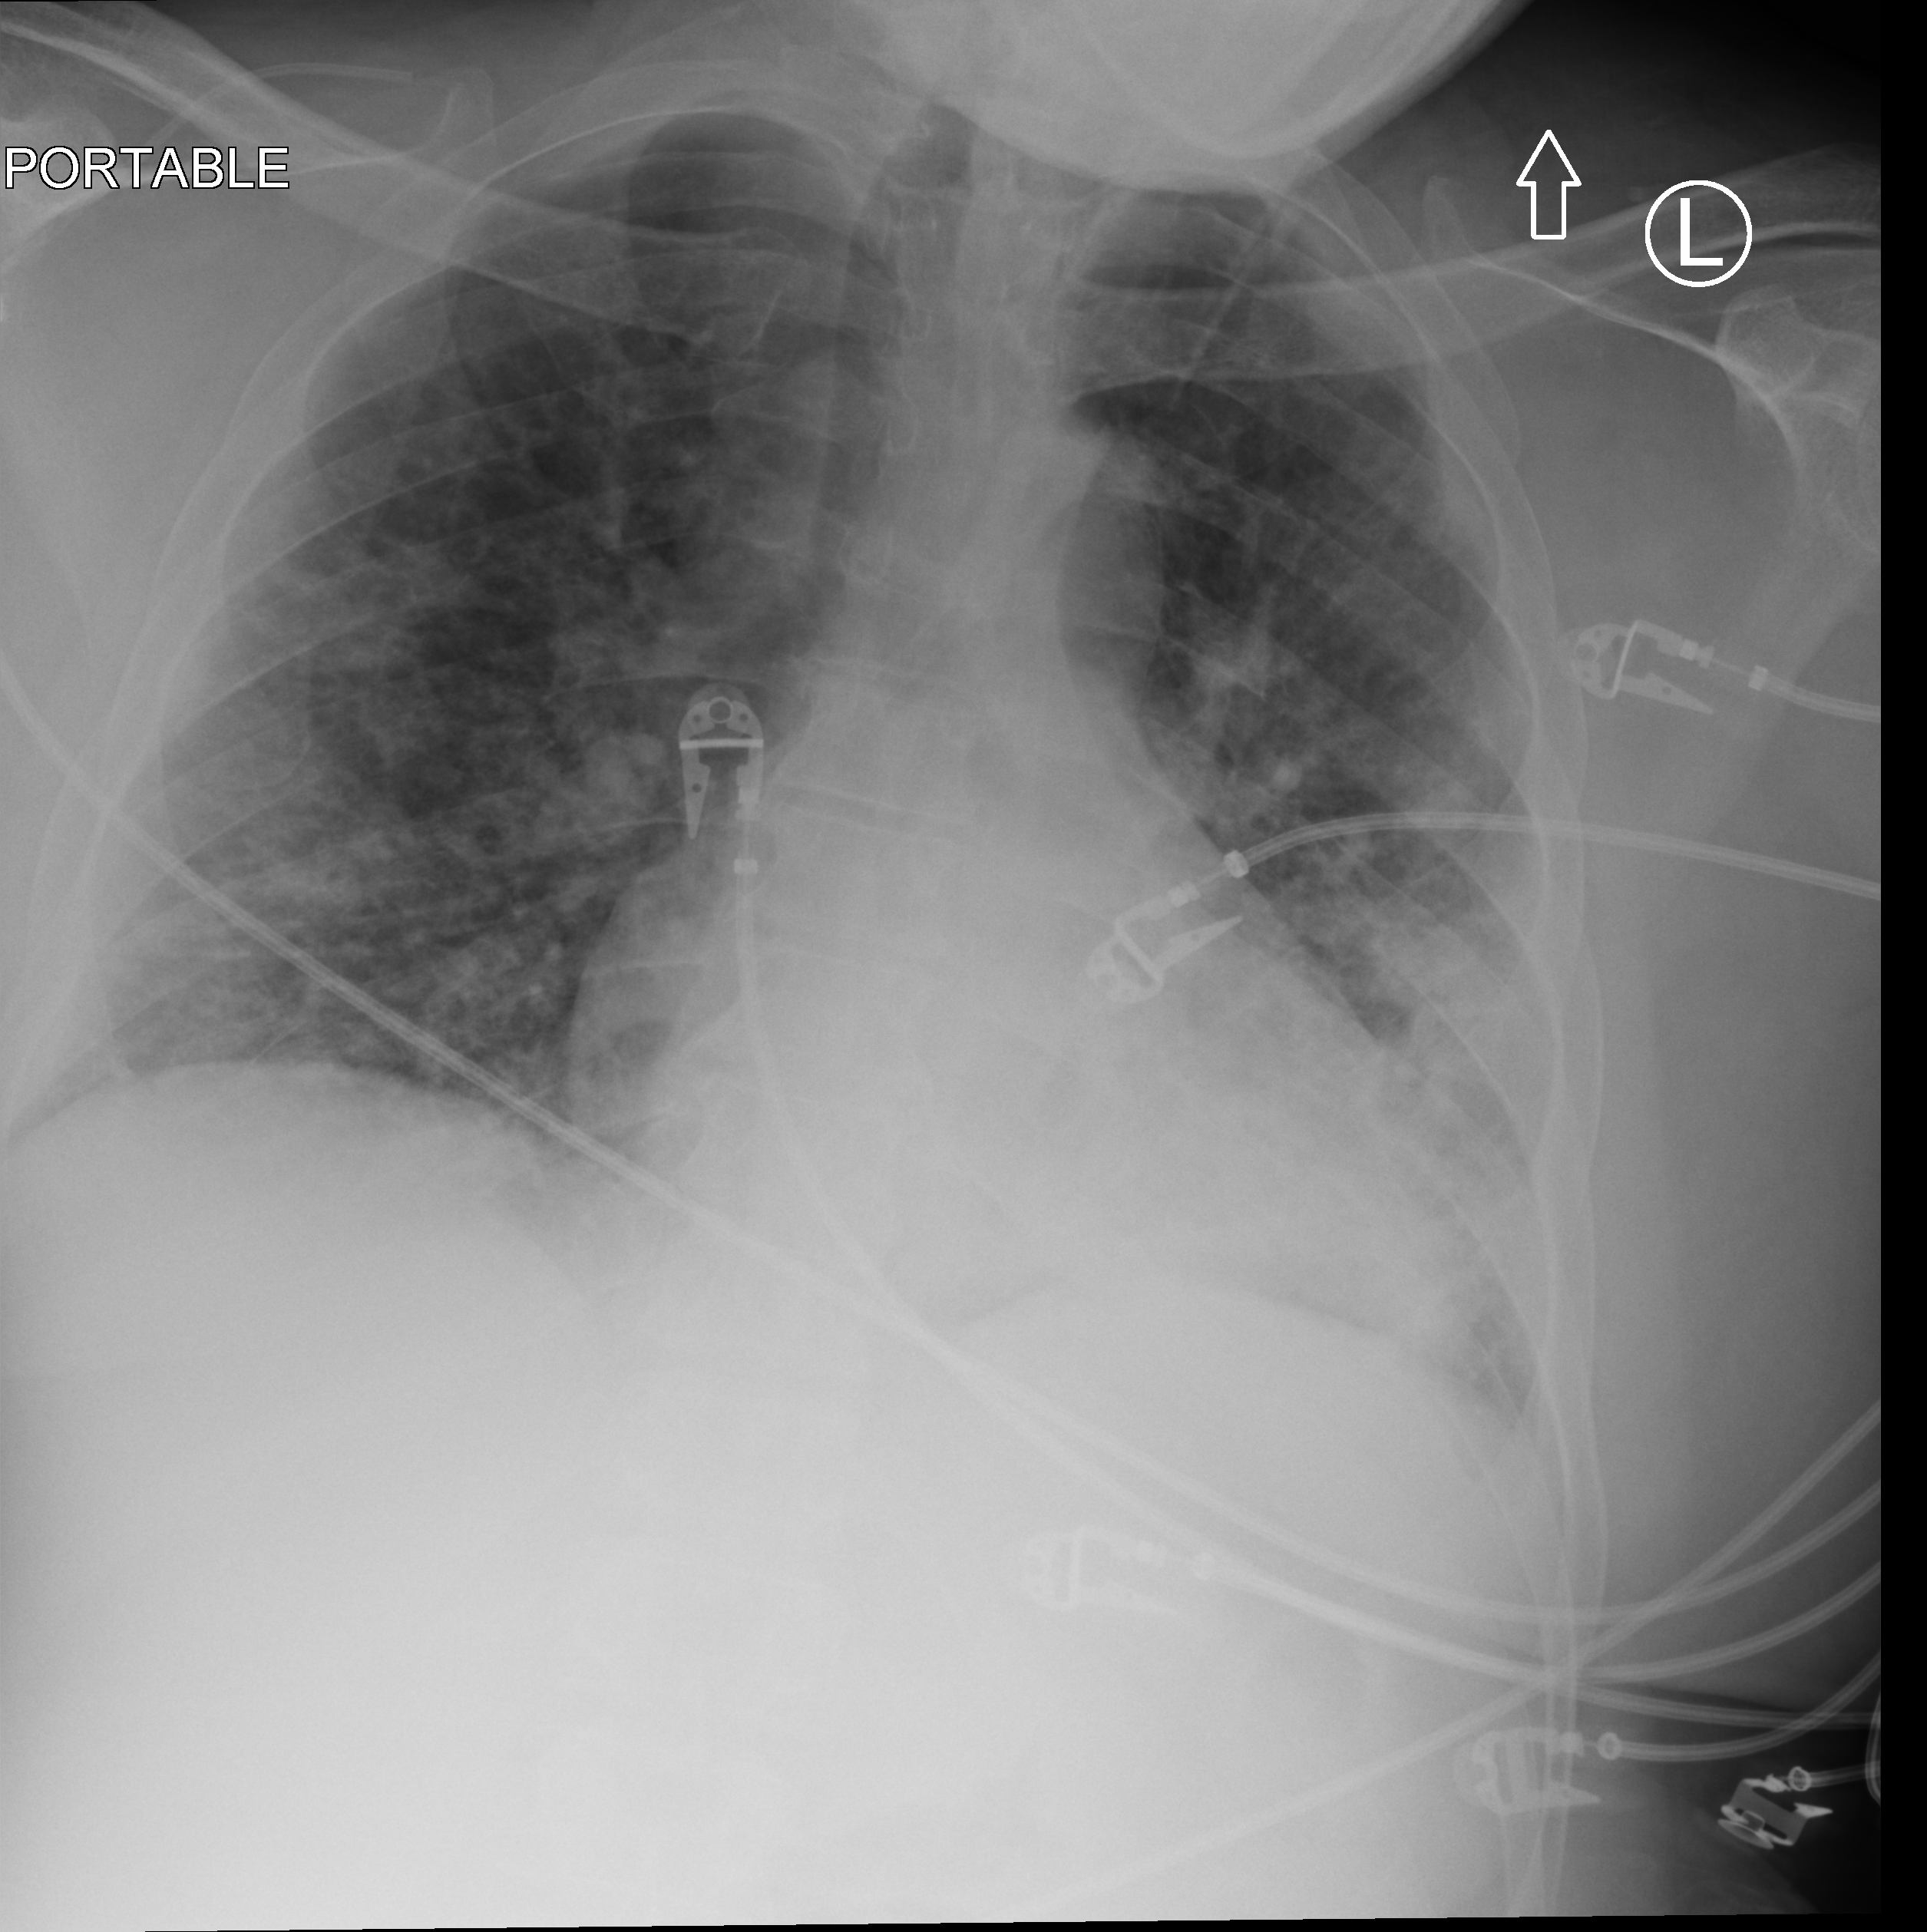
Chest X-ray (portable), anteroposterior (AP) projection. Patient hospitalised with COVID-19; male, aged 18–59 years.
From the hospital-stay record, not from the radiograph (when in the stay this image was taken is not recorded):
- chronic kidney disease (admission record): no
- admitted to intensive care during this hospital stay: yes